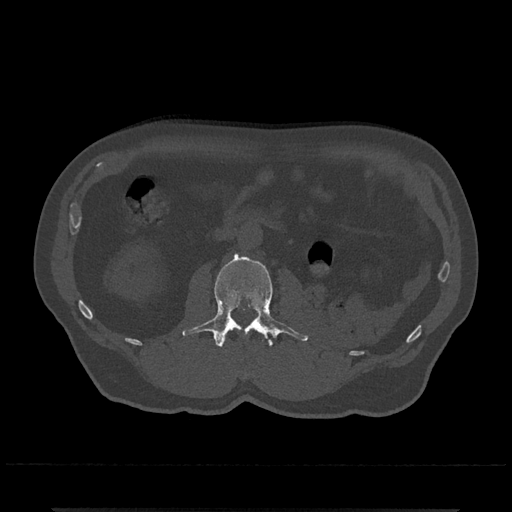
CT including the spine, one axial slice. Slice 297 of 797 in the series (ordered by position). Reconstruction kernel Br40s/3. Bone window (W 1800 / L 400 HU). 0.5 mm slice thickness. 512 × 512 image matrix, field of view 393 × 393 mm. Patient: male, 67 years. From the clinical record (not read from this slice): primary cancer: prostate.
Annotated regions visible in this slice (semi-automatically segmented with operator editing):
- L2 vertebra: box from (x=182, y=253) to (x=309, y=347) px